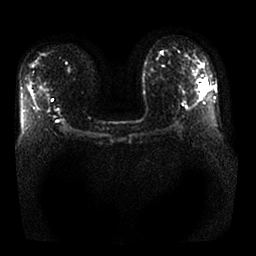
Breast MRI, one axial slice. Slice 17 of 25 in the series (ordered by position). Diffusion-weighted series; image 2 of 4 stored at this slice position (different b-values; order by instance number). 1.5 T. 4 mm slice thickness. 256 × 256 image matrix, field of view 360 × 360 mm. Female patient.
Outlined on this slice (outlined manually by an expert reader):
- tumour on diffusion-weighted imaging: bounding box <200,79,207,92> (left, top, right, bottom; pixels)